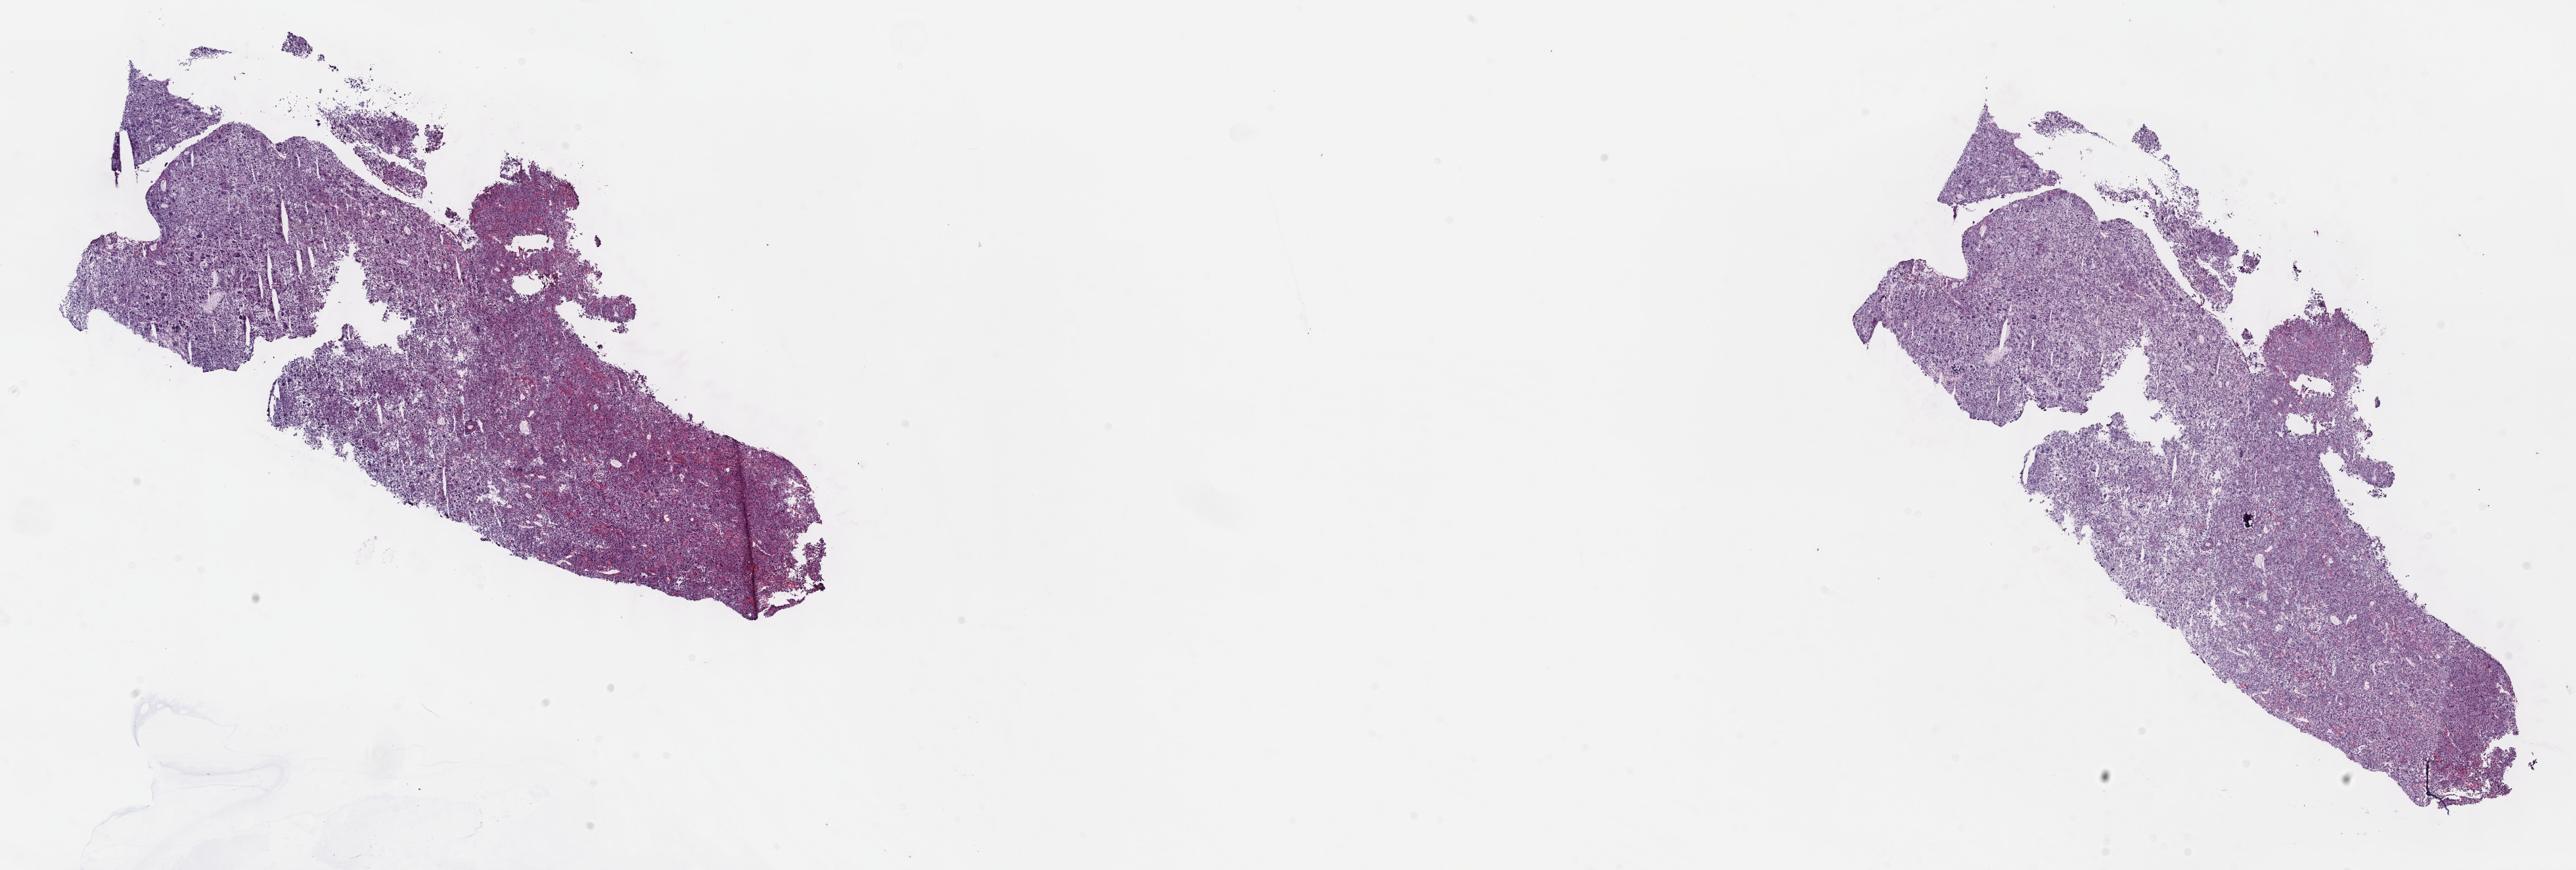
Digitized H&E-stained tissue section (whole slide), shown as a low-resolution overview of the whole scanned area (about 31.7 x 10.7 mm); frozen section; primary tumour sample from the connective, subcutaneous and other soft tissues. Patient: male, age at initial diagnosis 56 years. Slide review estimates, as recorded: tumour cells 100%, tumour nuclei 80%, normal cells 0%, stromal cells 0%, necrosis 0%. Infiltration values recorded for this section: lymphocyte infiltration 2%, monocyte infiltration 0%, neutrophil infiltration 0%.
Diagnosis: Undifferentiated sarcoma.